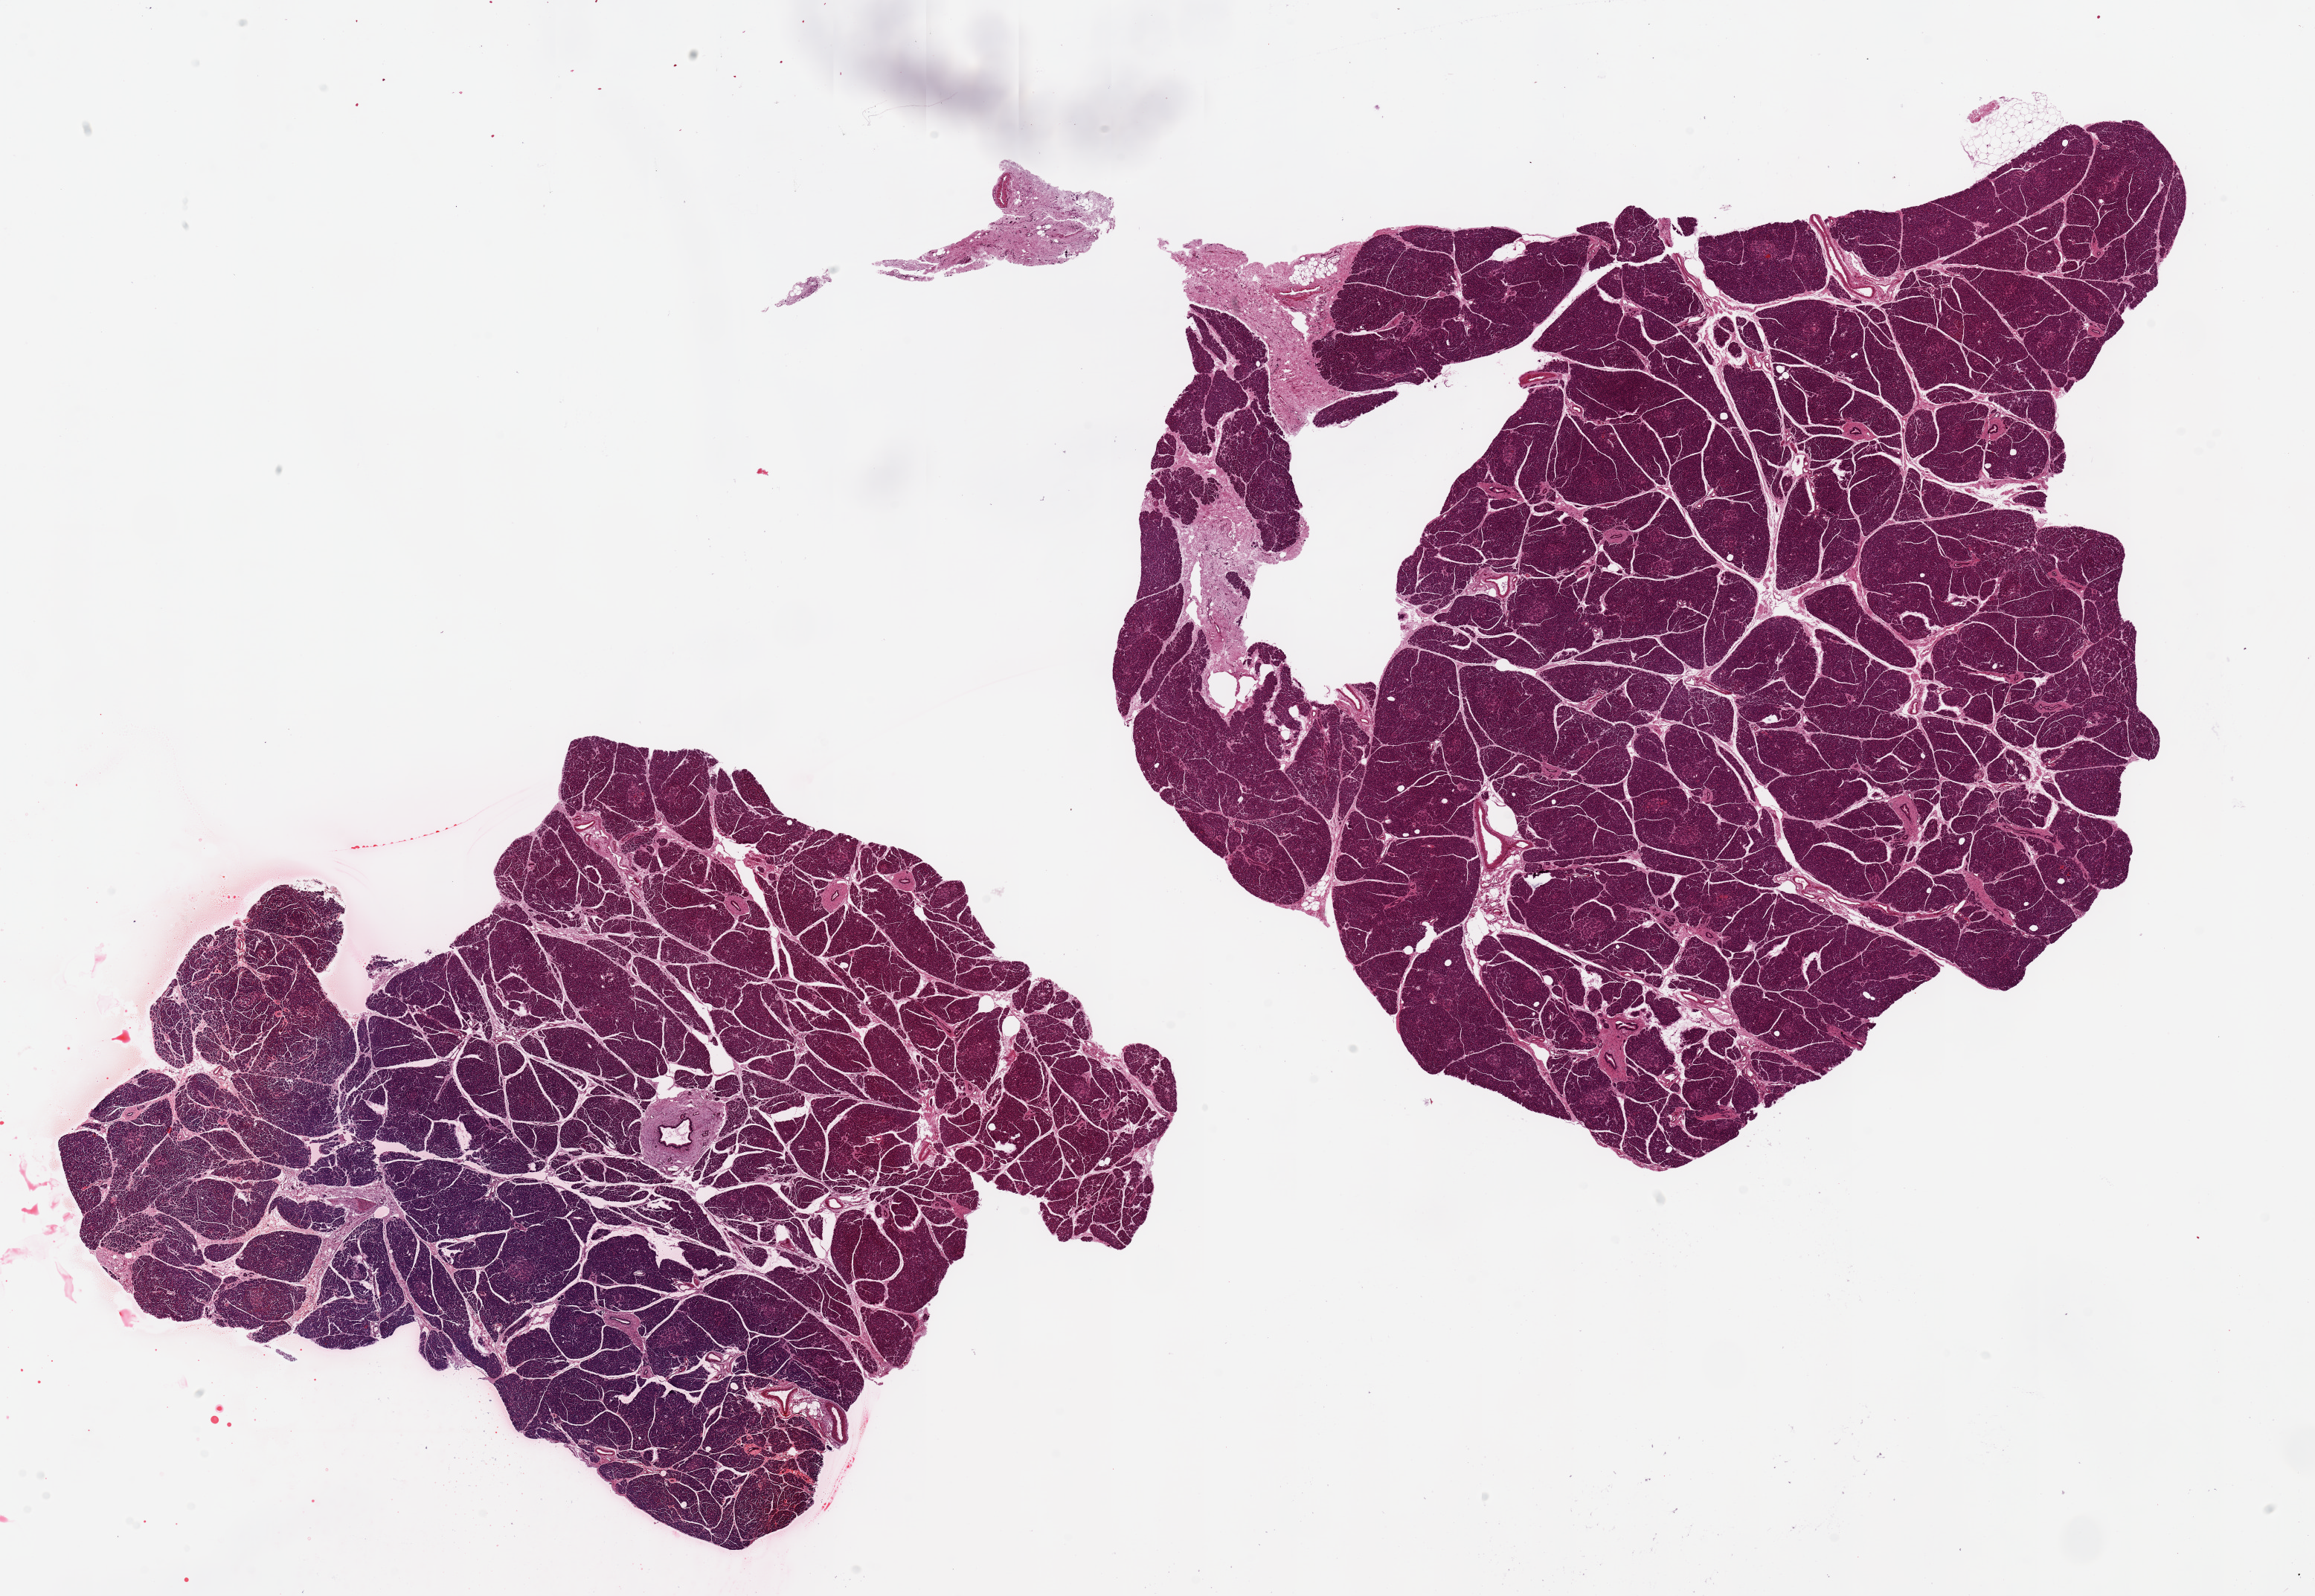
Digitized haematoxylin and eosin-stained section — shown as a low-resolution overview of the whole scanned area (about 24.6 x 17.0 mm, from a 20x scan). PAXgene-fixed, paraffin-embedded tissue. Sampled site (target tissue): pancreas. Donor tissue sample. Donor: male.
Review note (as recorded): 2 pieces ~11x8mm; Extremely well-preserved, no adherent fat; Well visualized Islets.